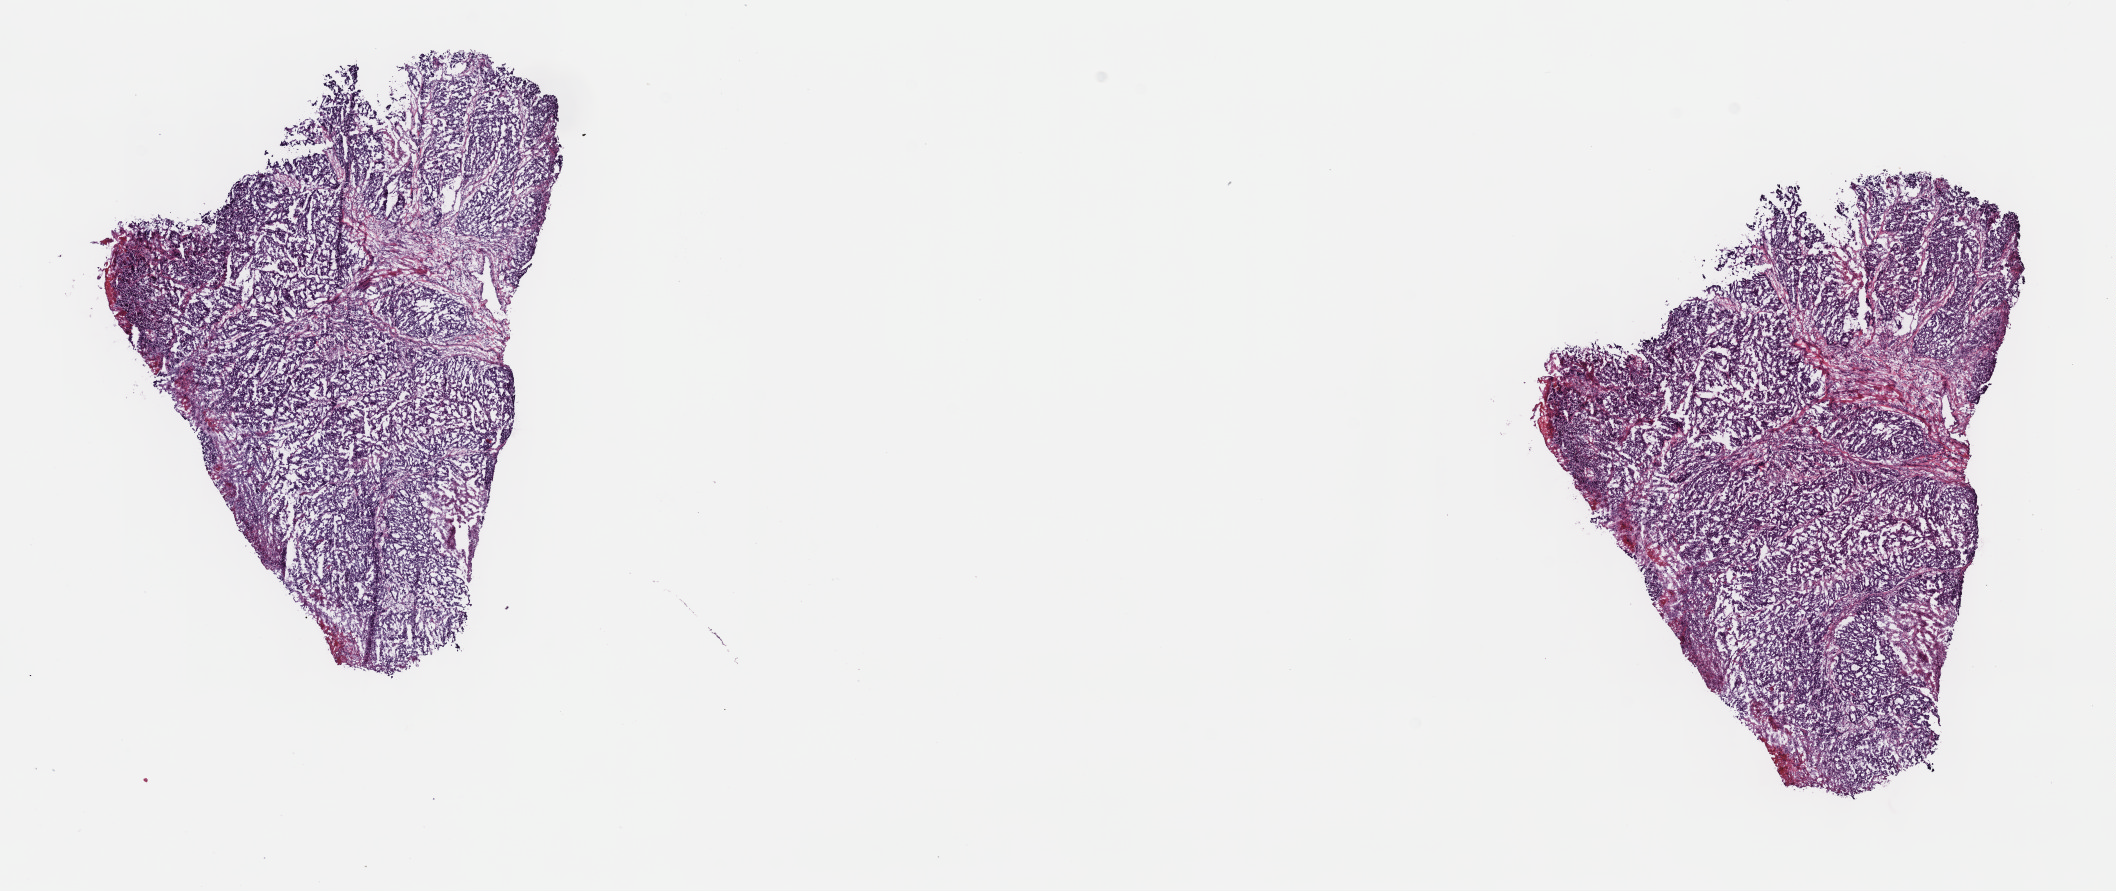
H&E whole-slide image, a low-resolution overview of the entire scanned area, about 17.1 x 7.2 mm (acquisition: 40x scan); frozen section from the top of the tissue portion; sample: primary tumour, stomach. Patient: female, age at initial diagnosis 52 years. Histologic grade: G2 (moderately differentiated). Composition of this section per pathologist review: tumour cells 98%, tumour nuclei 70%, normal cells 0%, stromal cells 0%, necrosis 2%. Inflammatory infiltration, as recorded: lymphocyte infiltration 3%, monocyte infiltration 0%, neutrophil infiltration 0%.
* lymph nodes positive (case pathology): 2 of 36 examined
* AJCC pathologic stage: IIIA (7th edition)
* diagnosis: Tubular adenocarcinoma (gastric antrum)